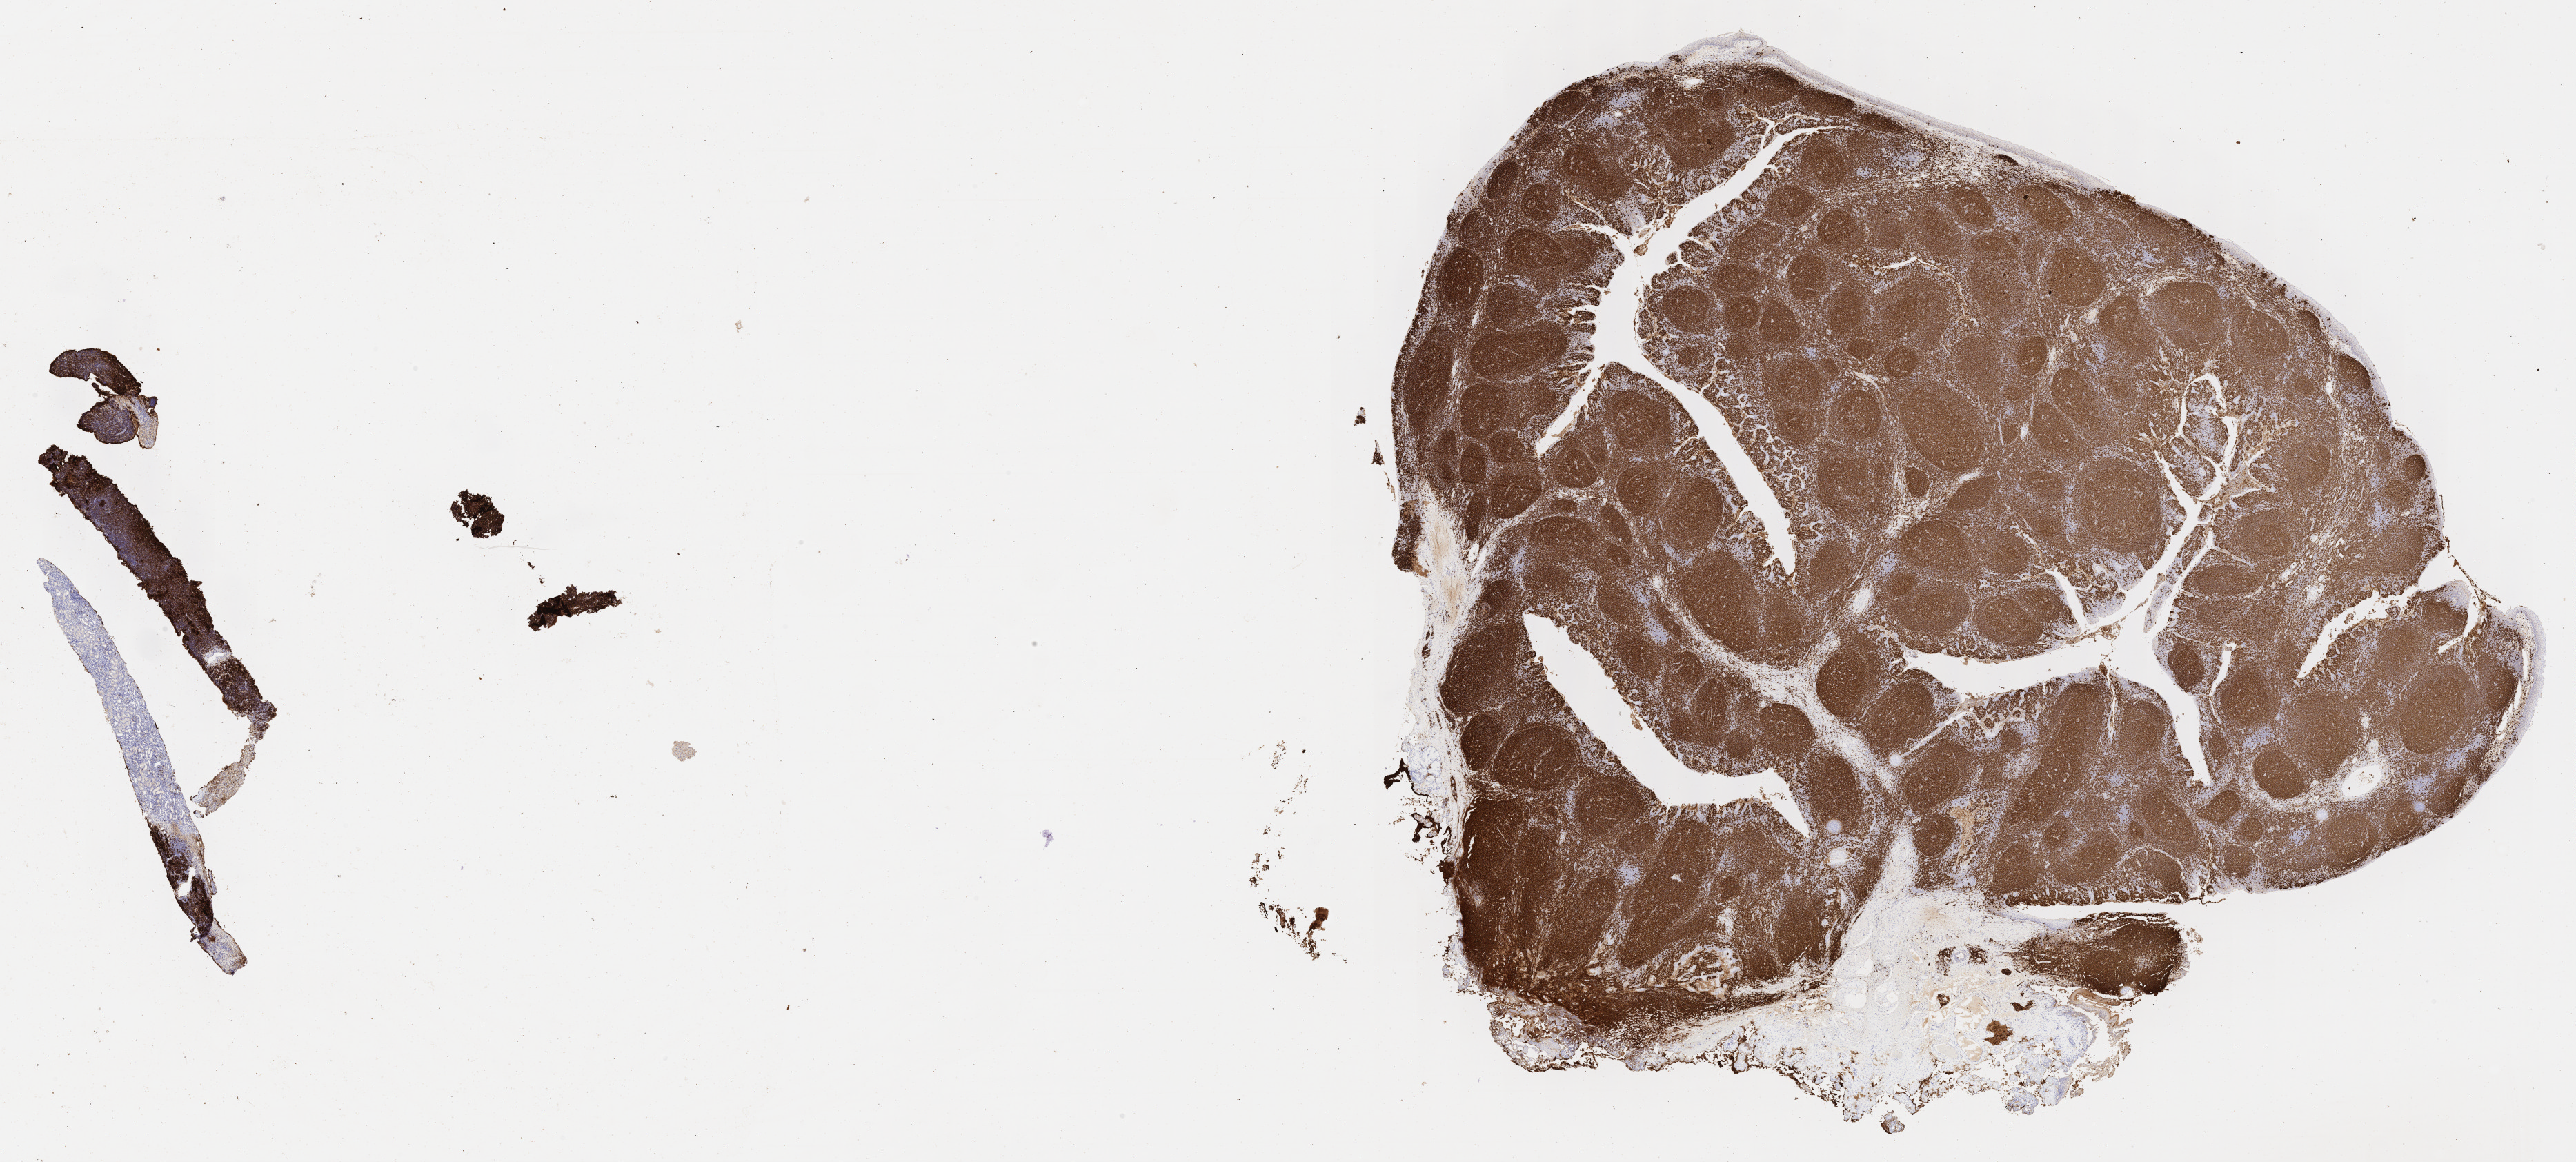
Immunohistochemistry (IHC) whole-slide image stained for CD20, whole scanned area (about 30.2 x 13.6 mm) shown as a low-resolution overview, specimen: tumor tissue, anatomic site: liver. Male, age 8 years at initial diagnosis.
• diagnosis: Burkitt lymphoma, NOS